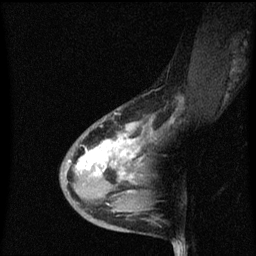
Breast MRI (dynamic contrast-enhanced), one sagittal slice. Position 29 of 60 along the scan axis. Dynamic contrast-enhanced series, image 2 of 3 at this slice position (ordered by acquisition). 1.5 T. TE 4.2 ms, TR 8.4 ms. 2 mm slice thickness. 256 × 256 image matrix, field of view 200 × 200 mm. Patient: female, 38 years. From the clinical record (not read from this slice): setting: breast cancer imaged before/during neoadjuvant chemotherapy; receptor status: HR-positive, HER2-negative.
Structures marked on this image (semi-automatically segmented with operator editing):
- analysis volume of interest (the breast-tissue region the enhancement analysis was run in; not a lesion): bounding box <60,114,151,205> (left, top, right, bottom; pixels)
- tumour enhancement mask (voxels above the 70 % enhancement threshold inside the analysis volume of interest): <76,124,141,179>